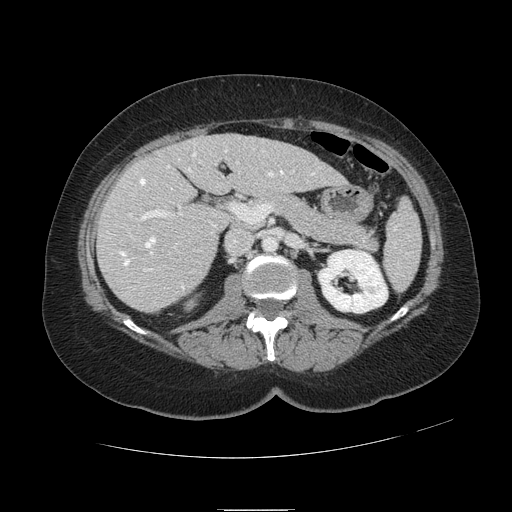
Contrast-enhanced abdominal CT, one axial slice. Slice 48 of 121 in the series (ordered by position). 120 kVp. Intravenous contrast given. Soft-tissue window (W 400 / L 40 HU). 512 × 512 image matrix, field of view 400 × 400 mm. Female patient, age 52 years. From the clinical record (not read from this slice): diagnosis: colorectal cancer liver metastases, imaged before liver resection; multiple liver metastases: yes; largest metastasis: 6.3 cm; disease in both lobes: no.
Outlined on this slice (expert manual segmentation):
- hepatic veins: bounding box (x1, y1, x2, y2) in pixels: (120, 150, 314, 289)
- liver: (98, 134, 344, 312)
- planned liver remnant (the part of the liver to remain after resection): (173, 134, 344, 196)
- portal vein (with intrahepatic branches): (129, 161, 294, 271)